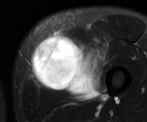
MRI of an extremity soft-tissue mass, one axial slice; T2-weighted fat-saturated; MR volume resampled by the dataset authors to the PET/CT grid (not the native acquisition matrix); 3.27 mm slice thickness; 147 × 122 image matrix, field of view 144 × 119 mm. Male patient. From the clinical record (not read from this slice): histological type: pleiomorphic liposarcoma; grade: high; site of the primary tumour: left thigh.
Structures marked on this image (expert contour drawn on MRI and transferred to this co-registered scan by the dataset authors):
- gross tumour volume including surrounding oedema: bounding box <32,30,104,102> (left, top, right, bottom; pixels)
- gross tumour volume (mass): <32,34,97,95>